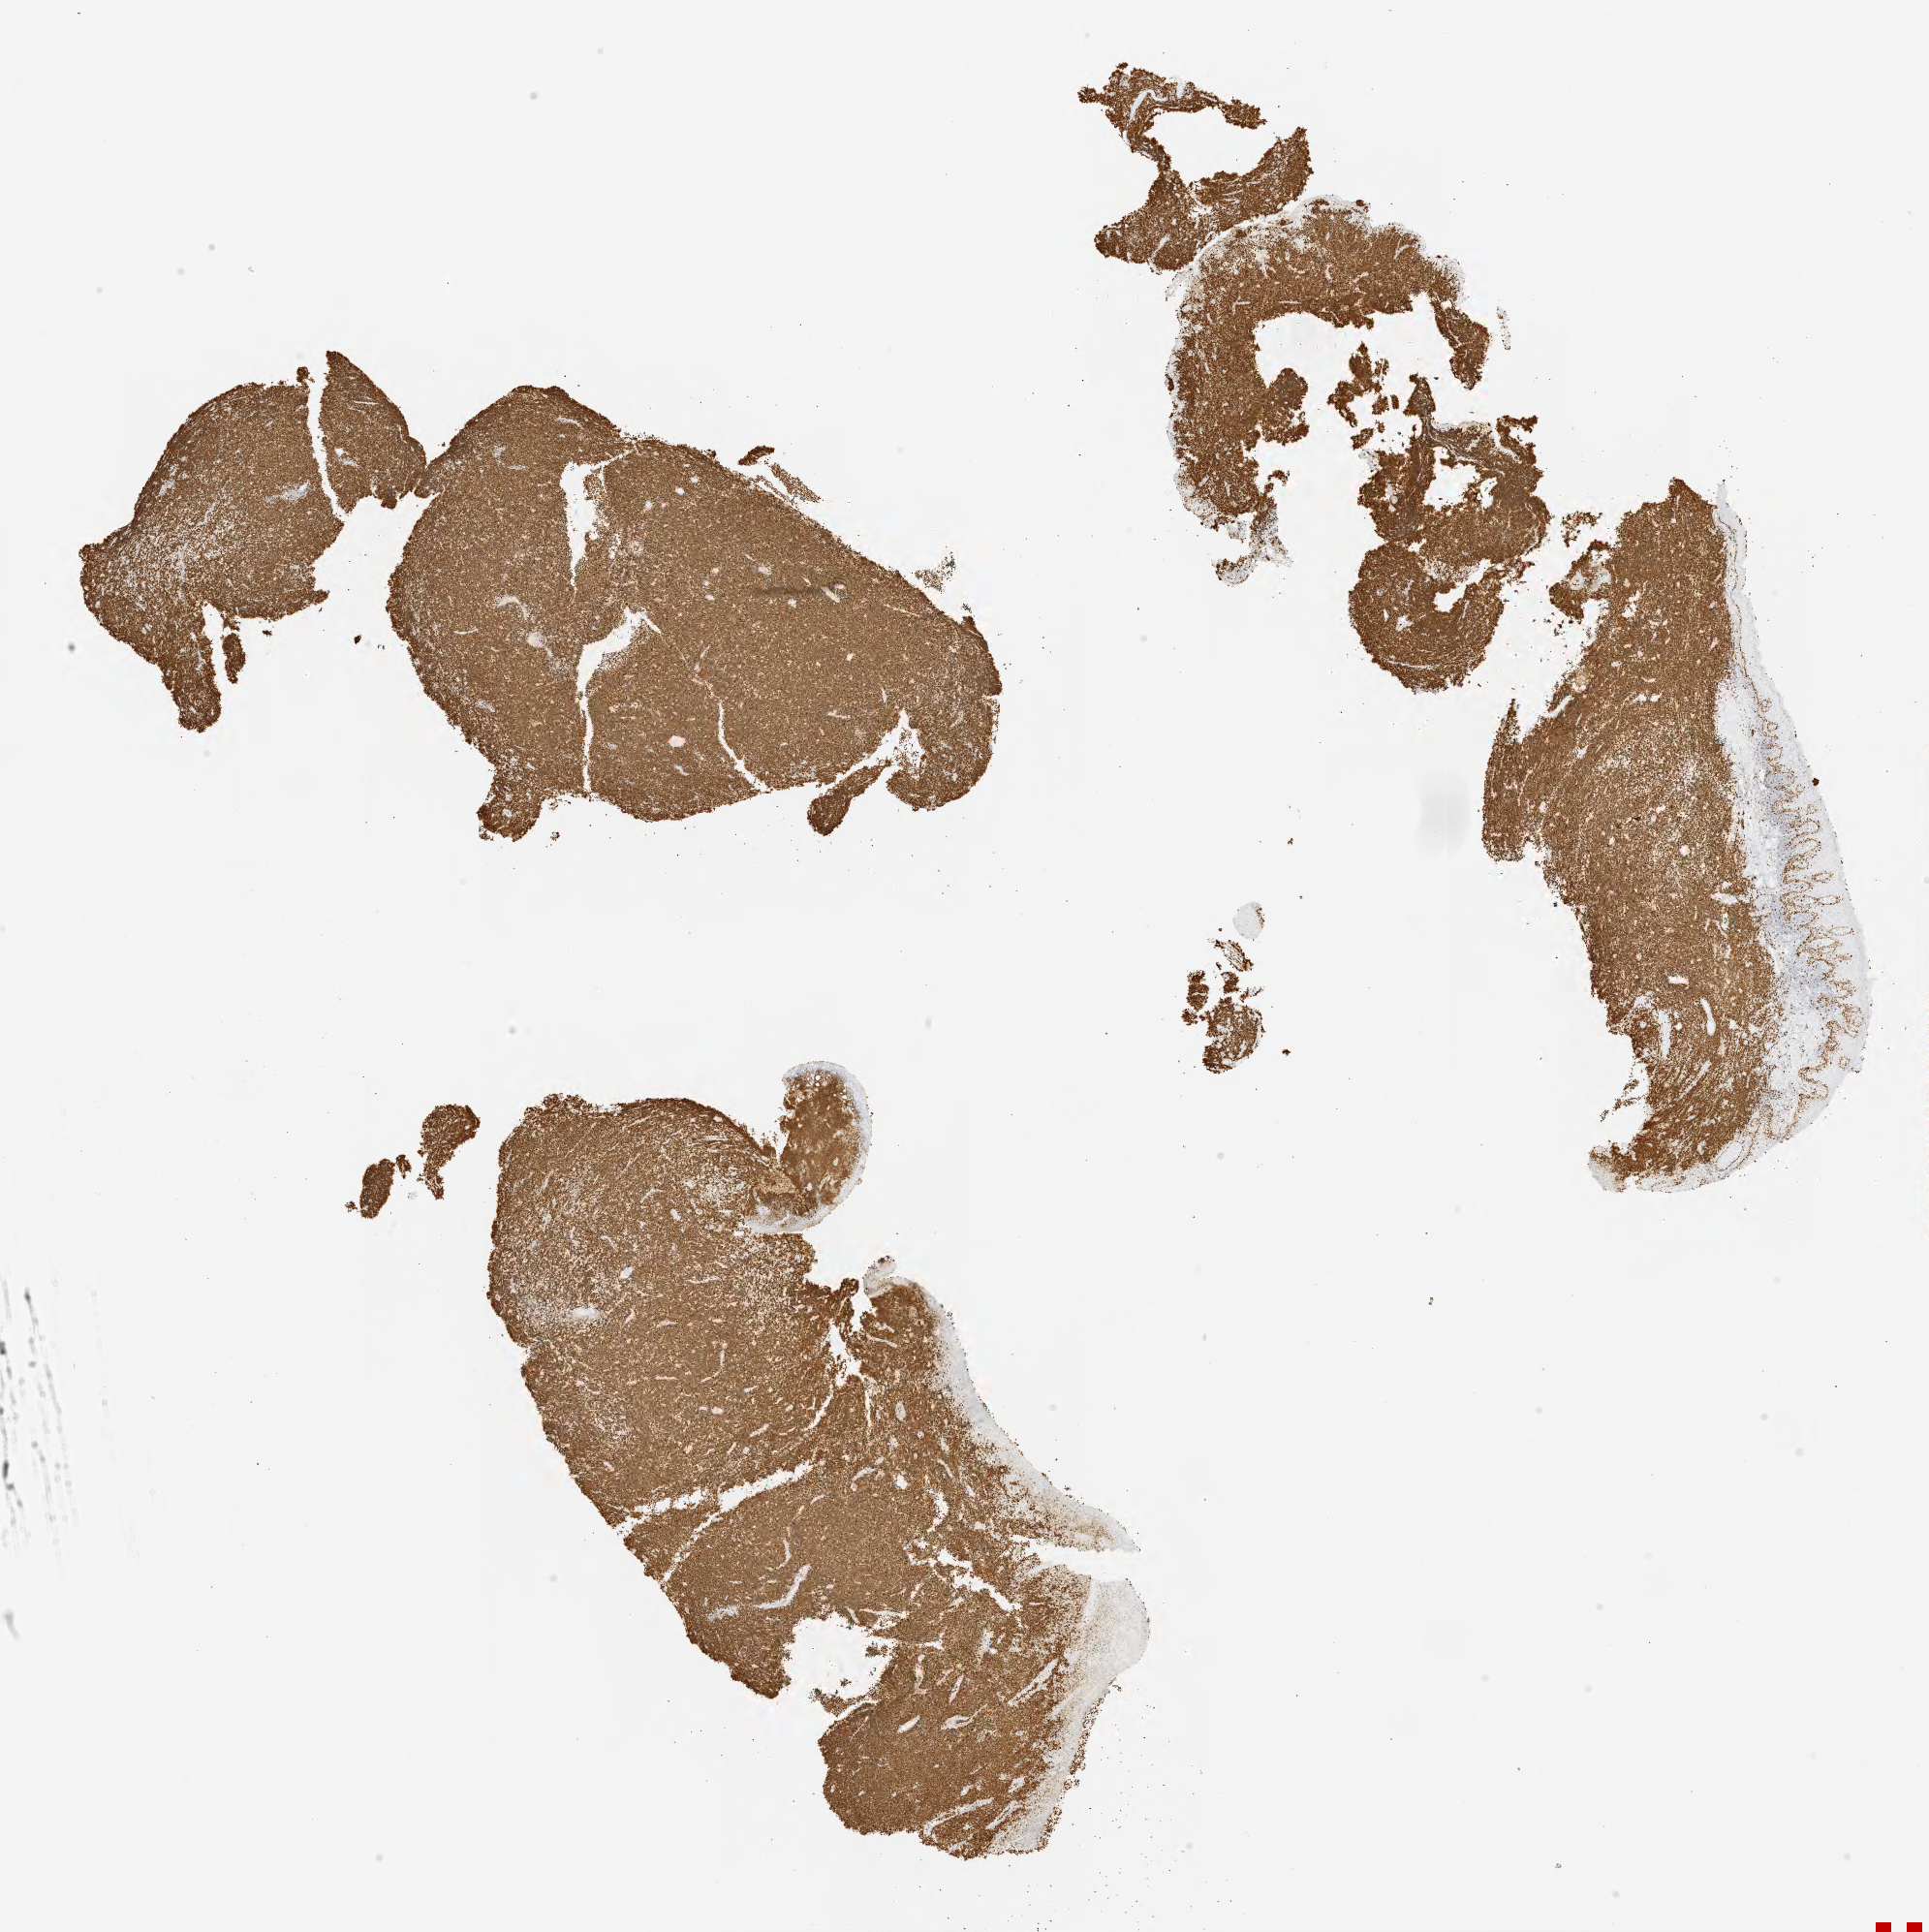
Whole-slide image, immunohistochemical stain for Ki-67 — a low-resolution overview of the entire scanned area, about 16.0 x 16.0 mm; specimen: tumor tissue. Male patient, 22 years old.
Diagnosis: Burkitt lymphoma, NOS.